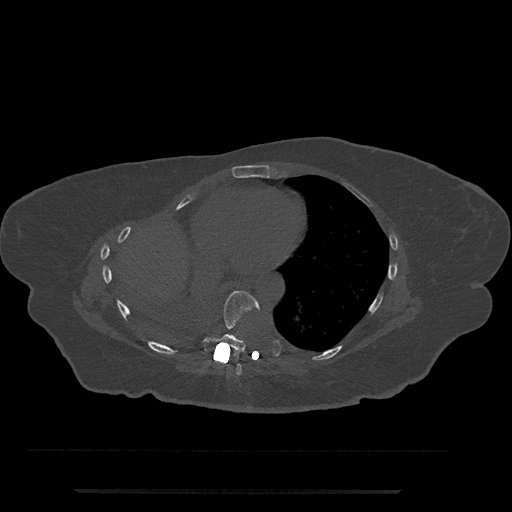
CT including the spine, one axial slice. Position 393 of 797 along the scan axis. Reconstruction kernel Br40s/3. Bone window (W 1800 / L 400 HU). 0.5 mm slice thickness. 512 × 512 image matrix. Female patient, age 51 years. From the clinical record (not read from this slice): primary cancer: neuro.
Structures marked on this image (semi-automatically segmented with operator editing):
- T7 vertebra: bounding box <233,364,242,376> (left, top, right, bottom; pixels)
- T8 vertebra: <203,291,260,352>